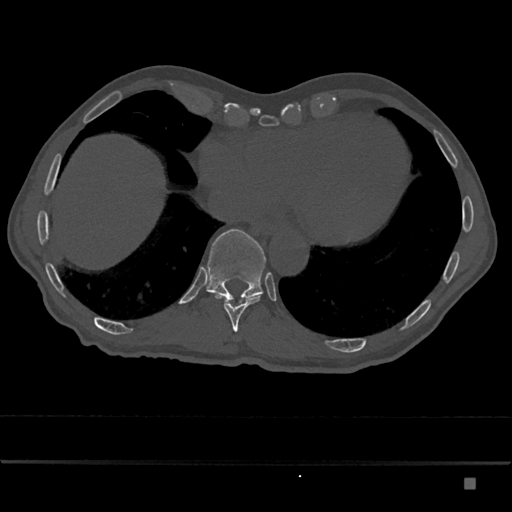
CT including the spine, one axial slice. Slice 713 of 797 in the series (ordered by position). Reconstruction kernel Br40s/3. 120 kVp. Bone window (W 1800 / L 400 HU). 0.5 mm slice thickness. 512 × 512 image matrix. Patient: male, 72 years. Case-level facts recorded for this patient, not image findings: primary cancer: prostate.
Structures marked on this image (semi-automatic segmentation, software-assisted and operator-edited):
- T10 vertebra: box from (x=216, y=296) to (x=260, y=333) px
- T11 vertebra: (x=204, y=229)–(x=266, y=301)